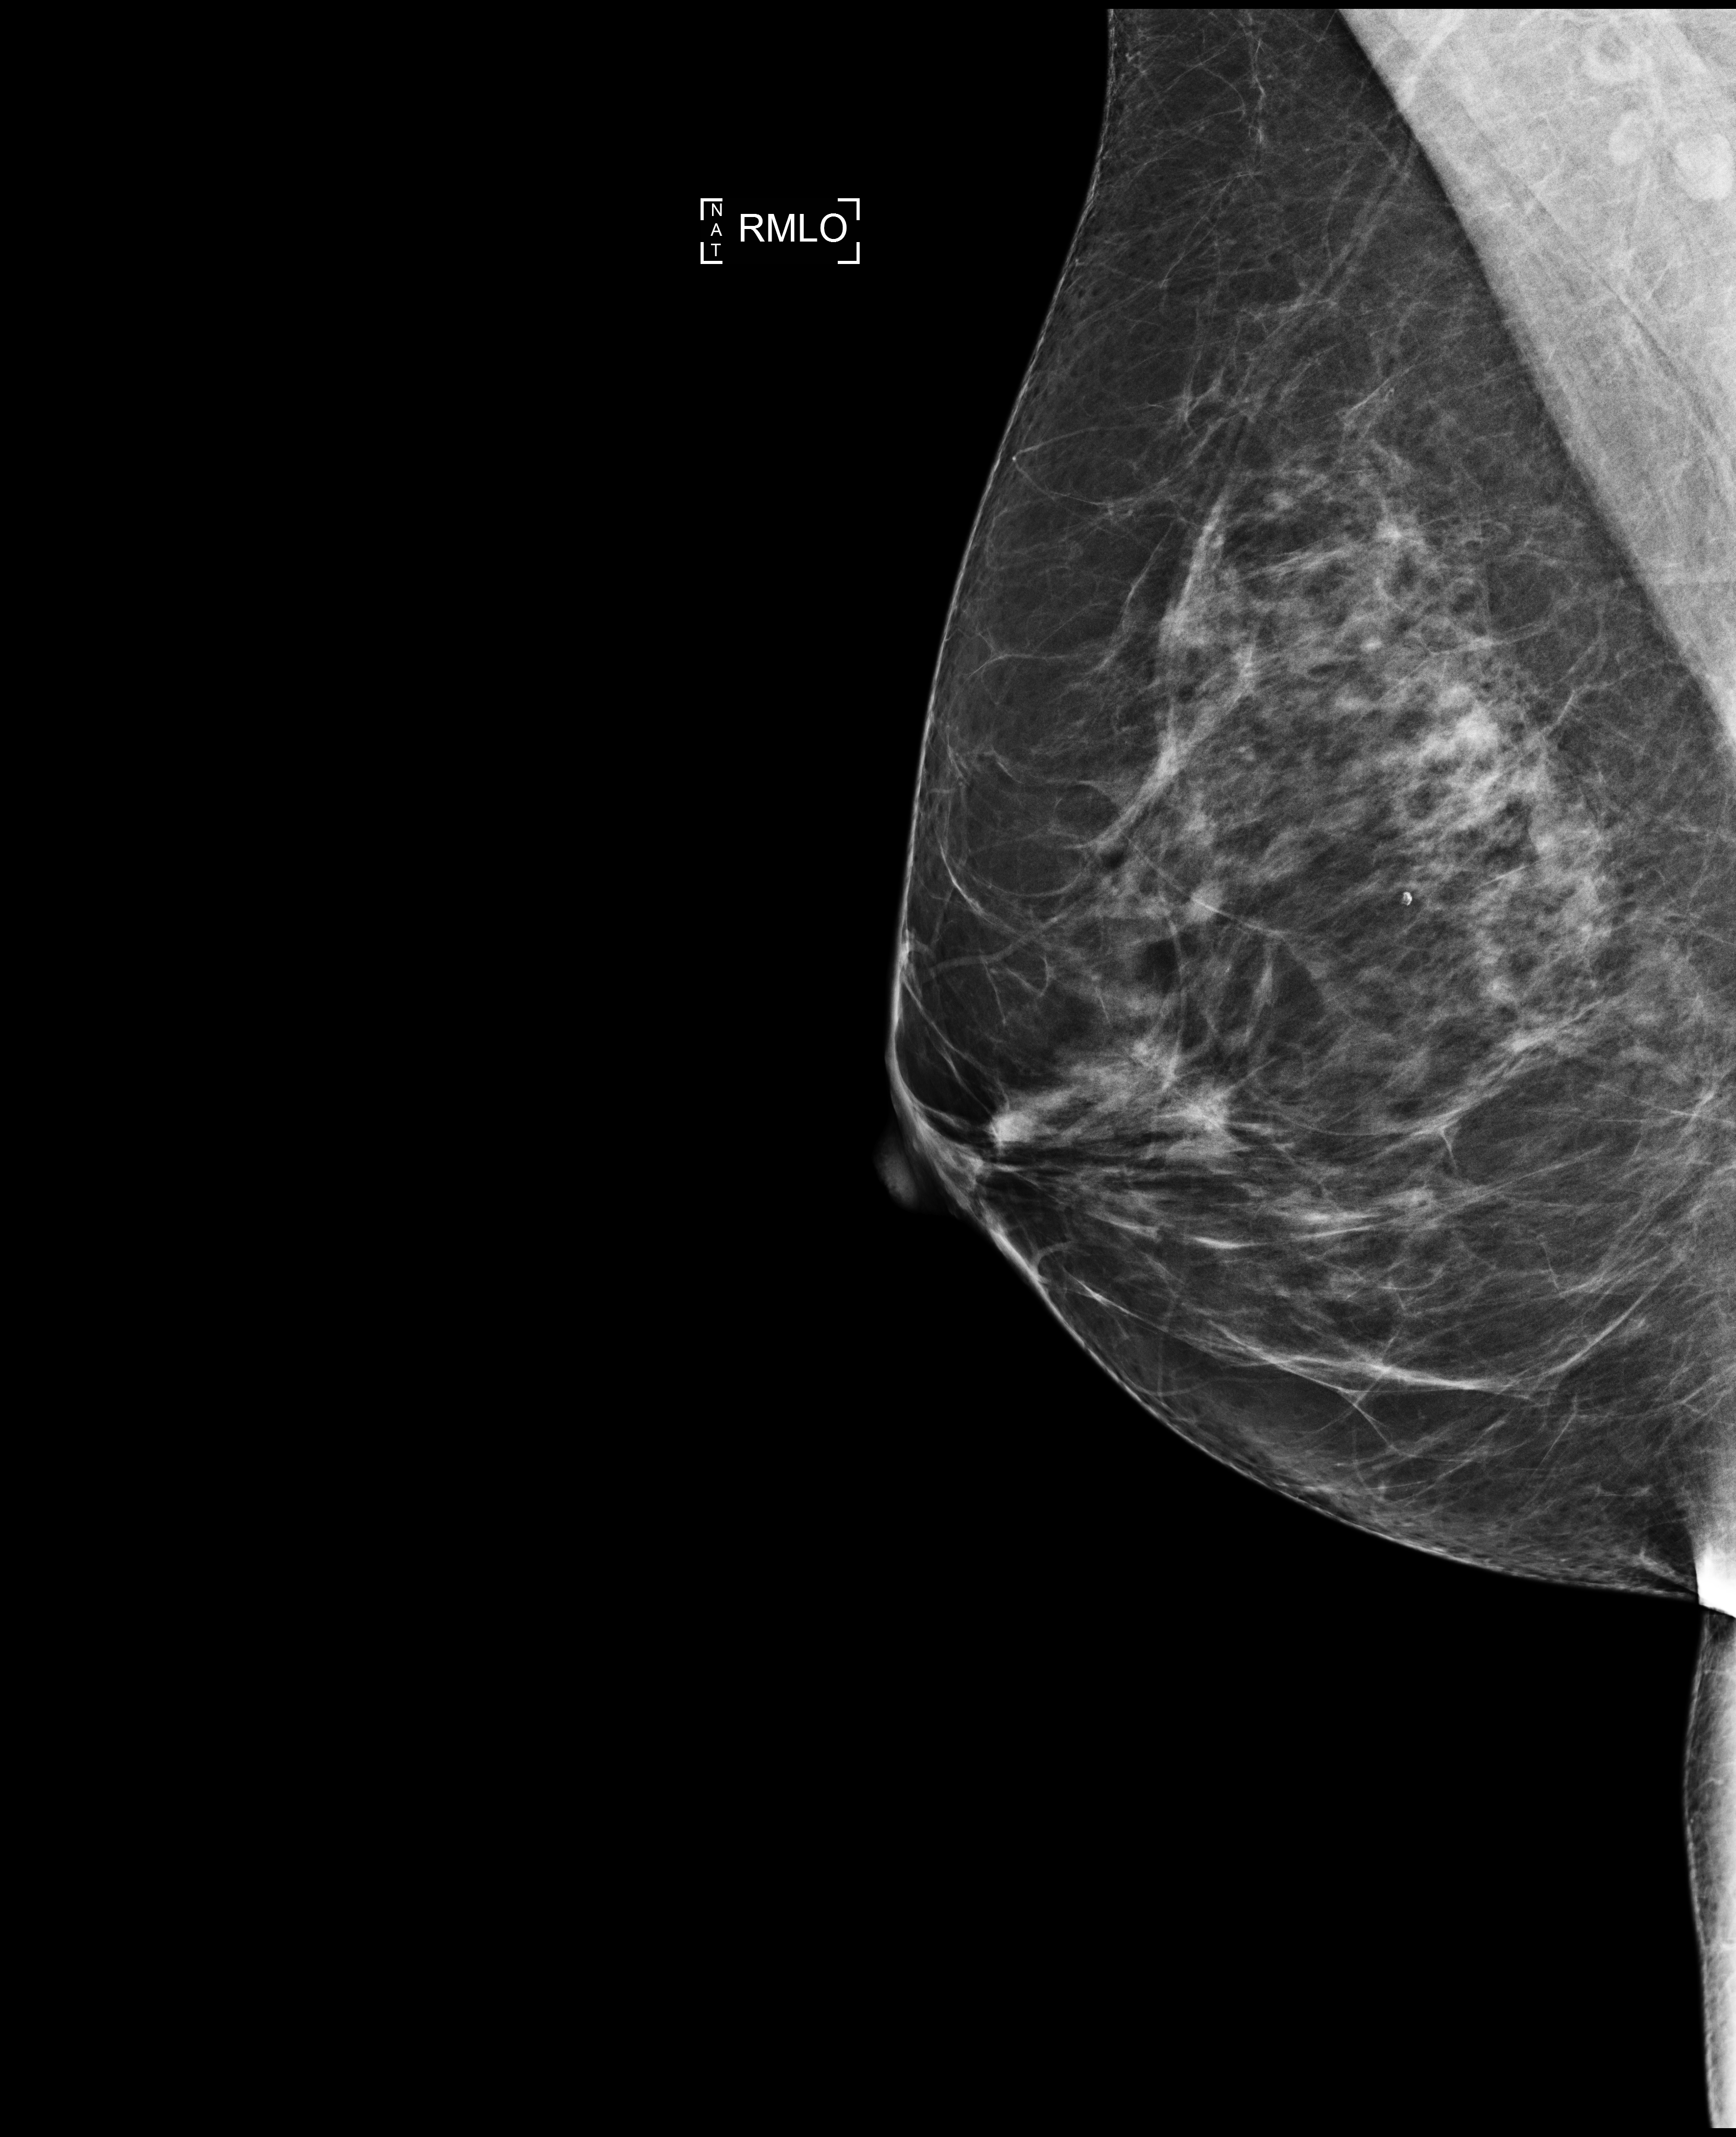
Full-field digital mammogram (FFDM); right breast; mediolateral oblique (MLO) view; screening examination. Patient aged 52 years (female).
BI-RADS breast density category at the screening exam (both breasts, scale 1–4): 2. Final BI-RADS category for the screening round (tomosynthesis exam, both breasts): category 1. Recall: no recall after this screen.